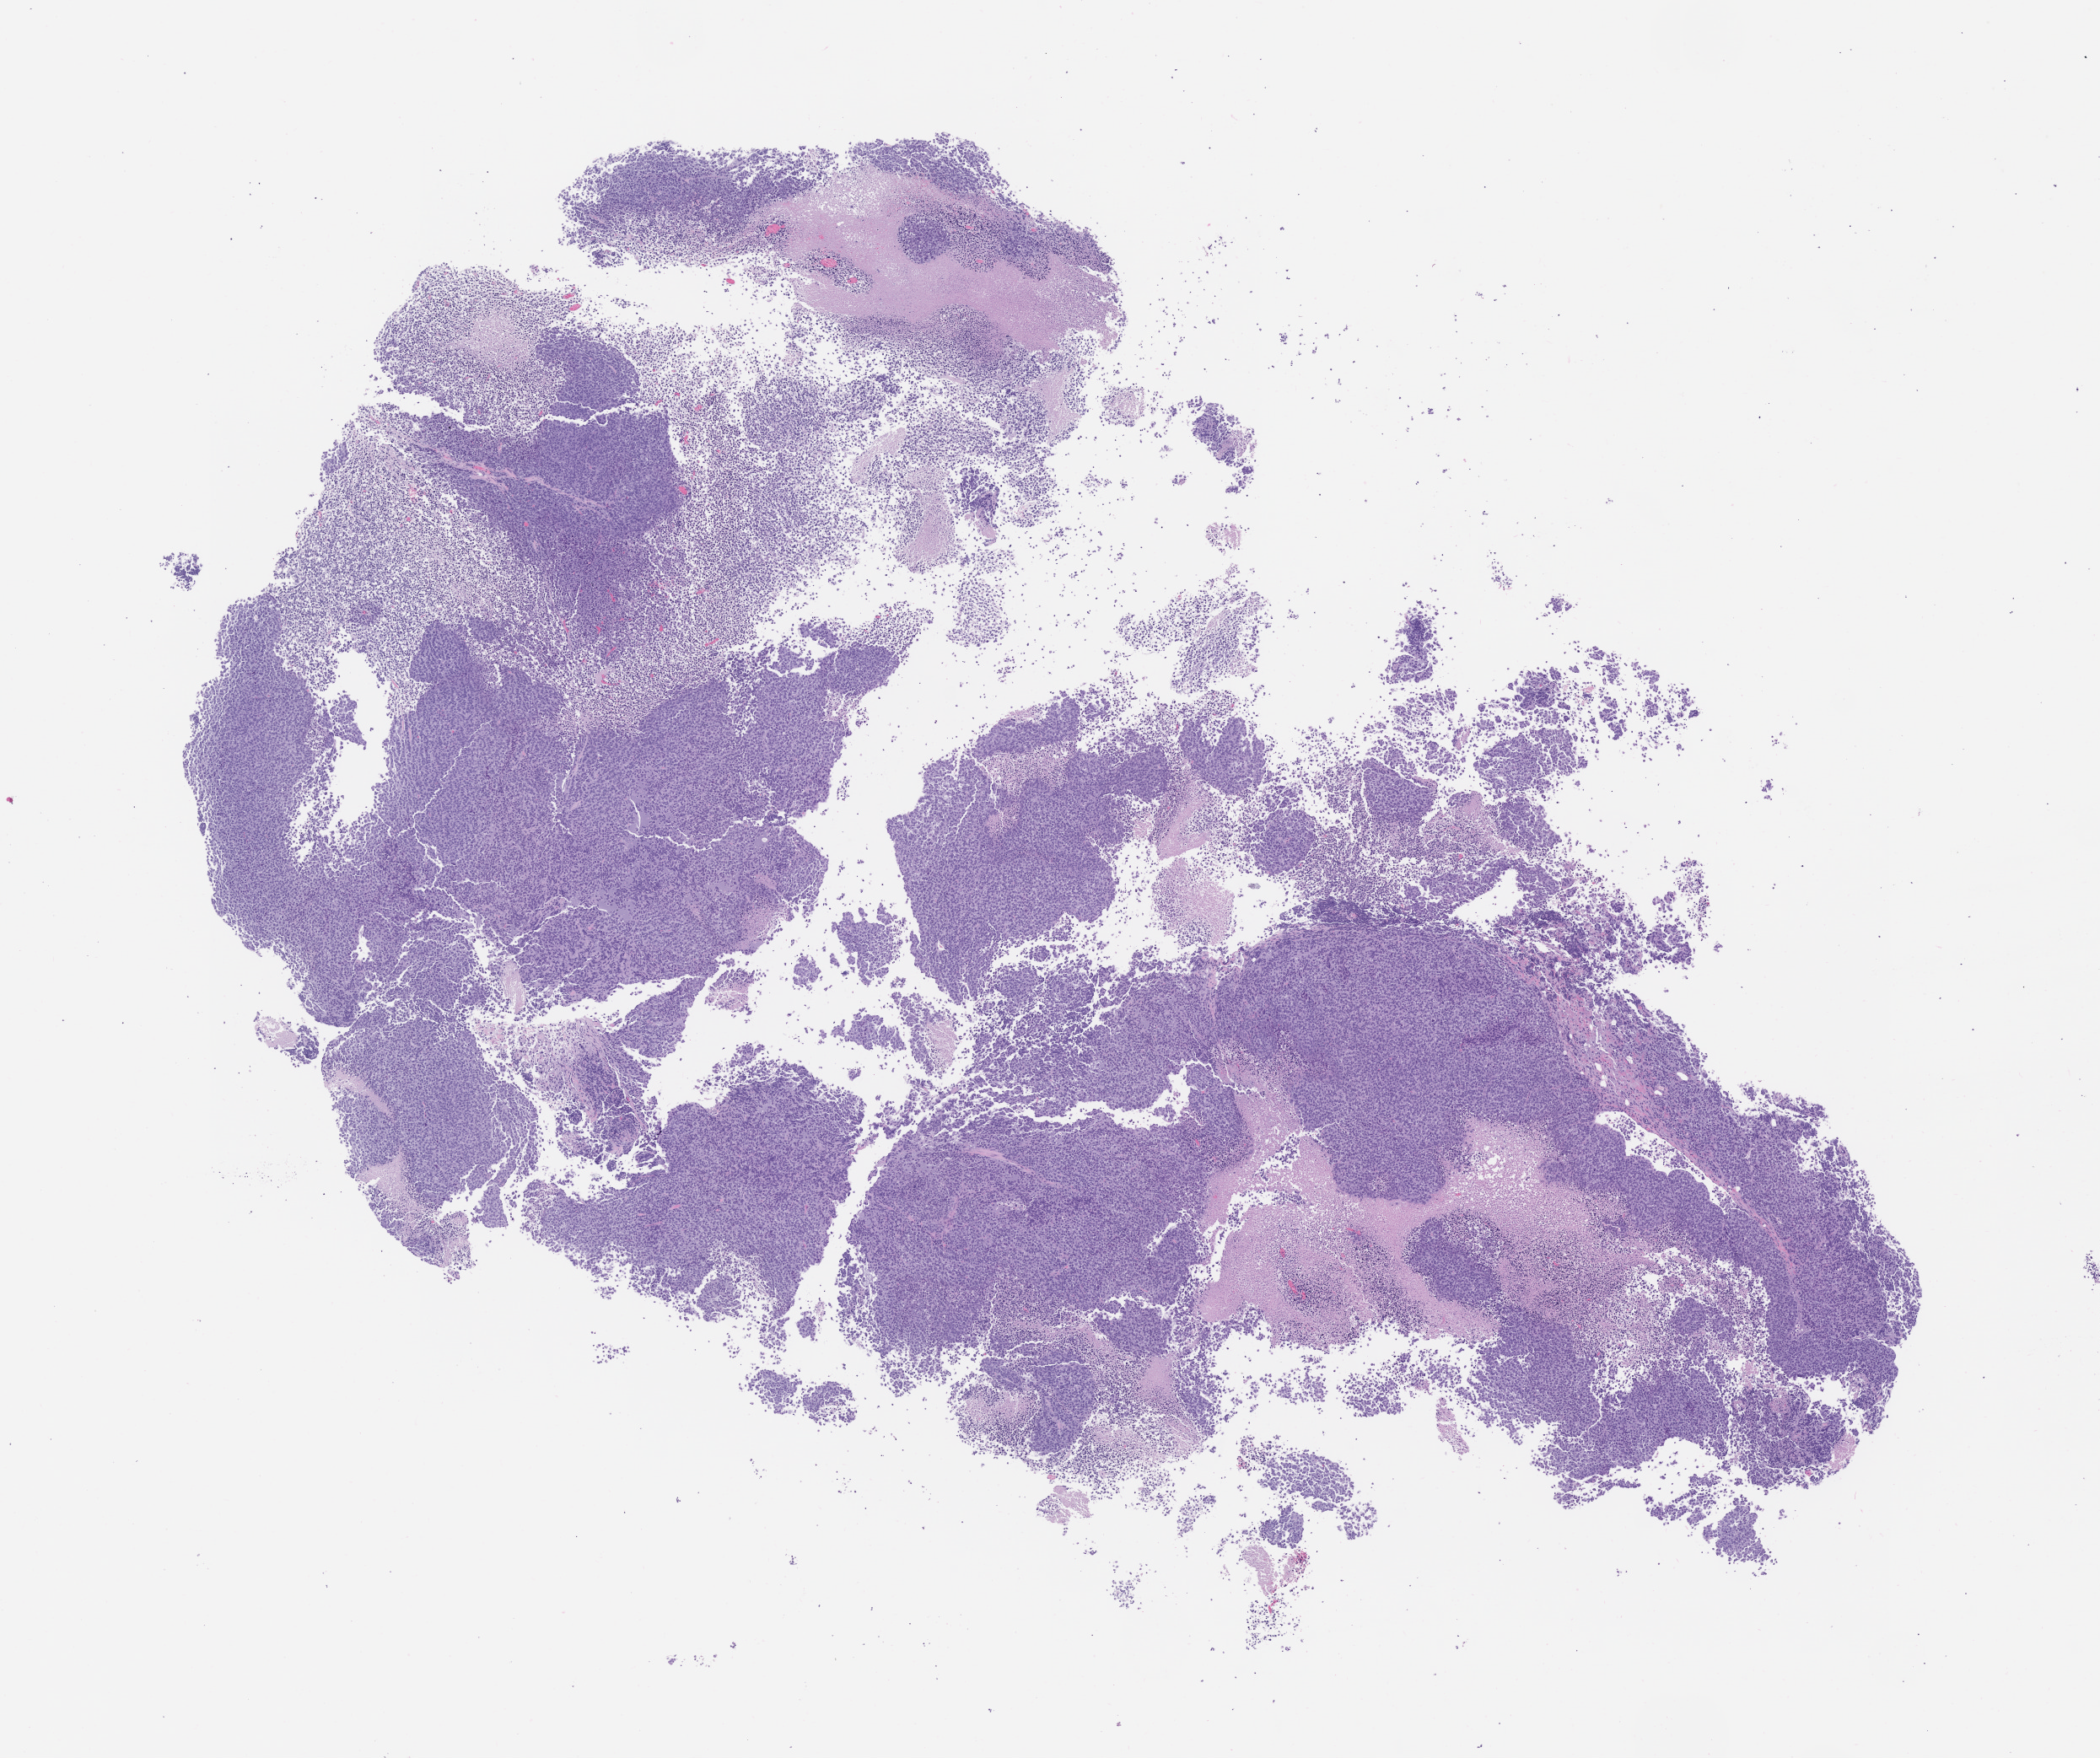
Whole-slide image, hematoxylin and eosin (H&E): patient-derived xenograft (human tumor grown in a mouse), passage 1 — shown as a low-resolution overview of the whole scanned area (about 10.0 x 8.4 mm). Formalin-fixed, paraffin-embedded (FFPE) tissue. Tumor site category: musculoskeletal.
Originating patient diagnosis: Ewing Sarcoma|Primitive Neuroectodermal Tumor.